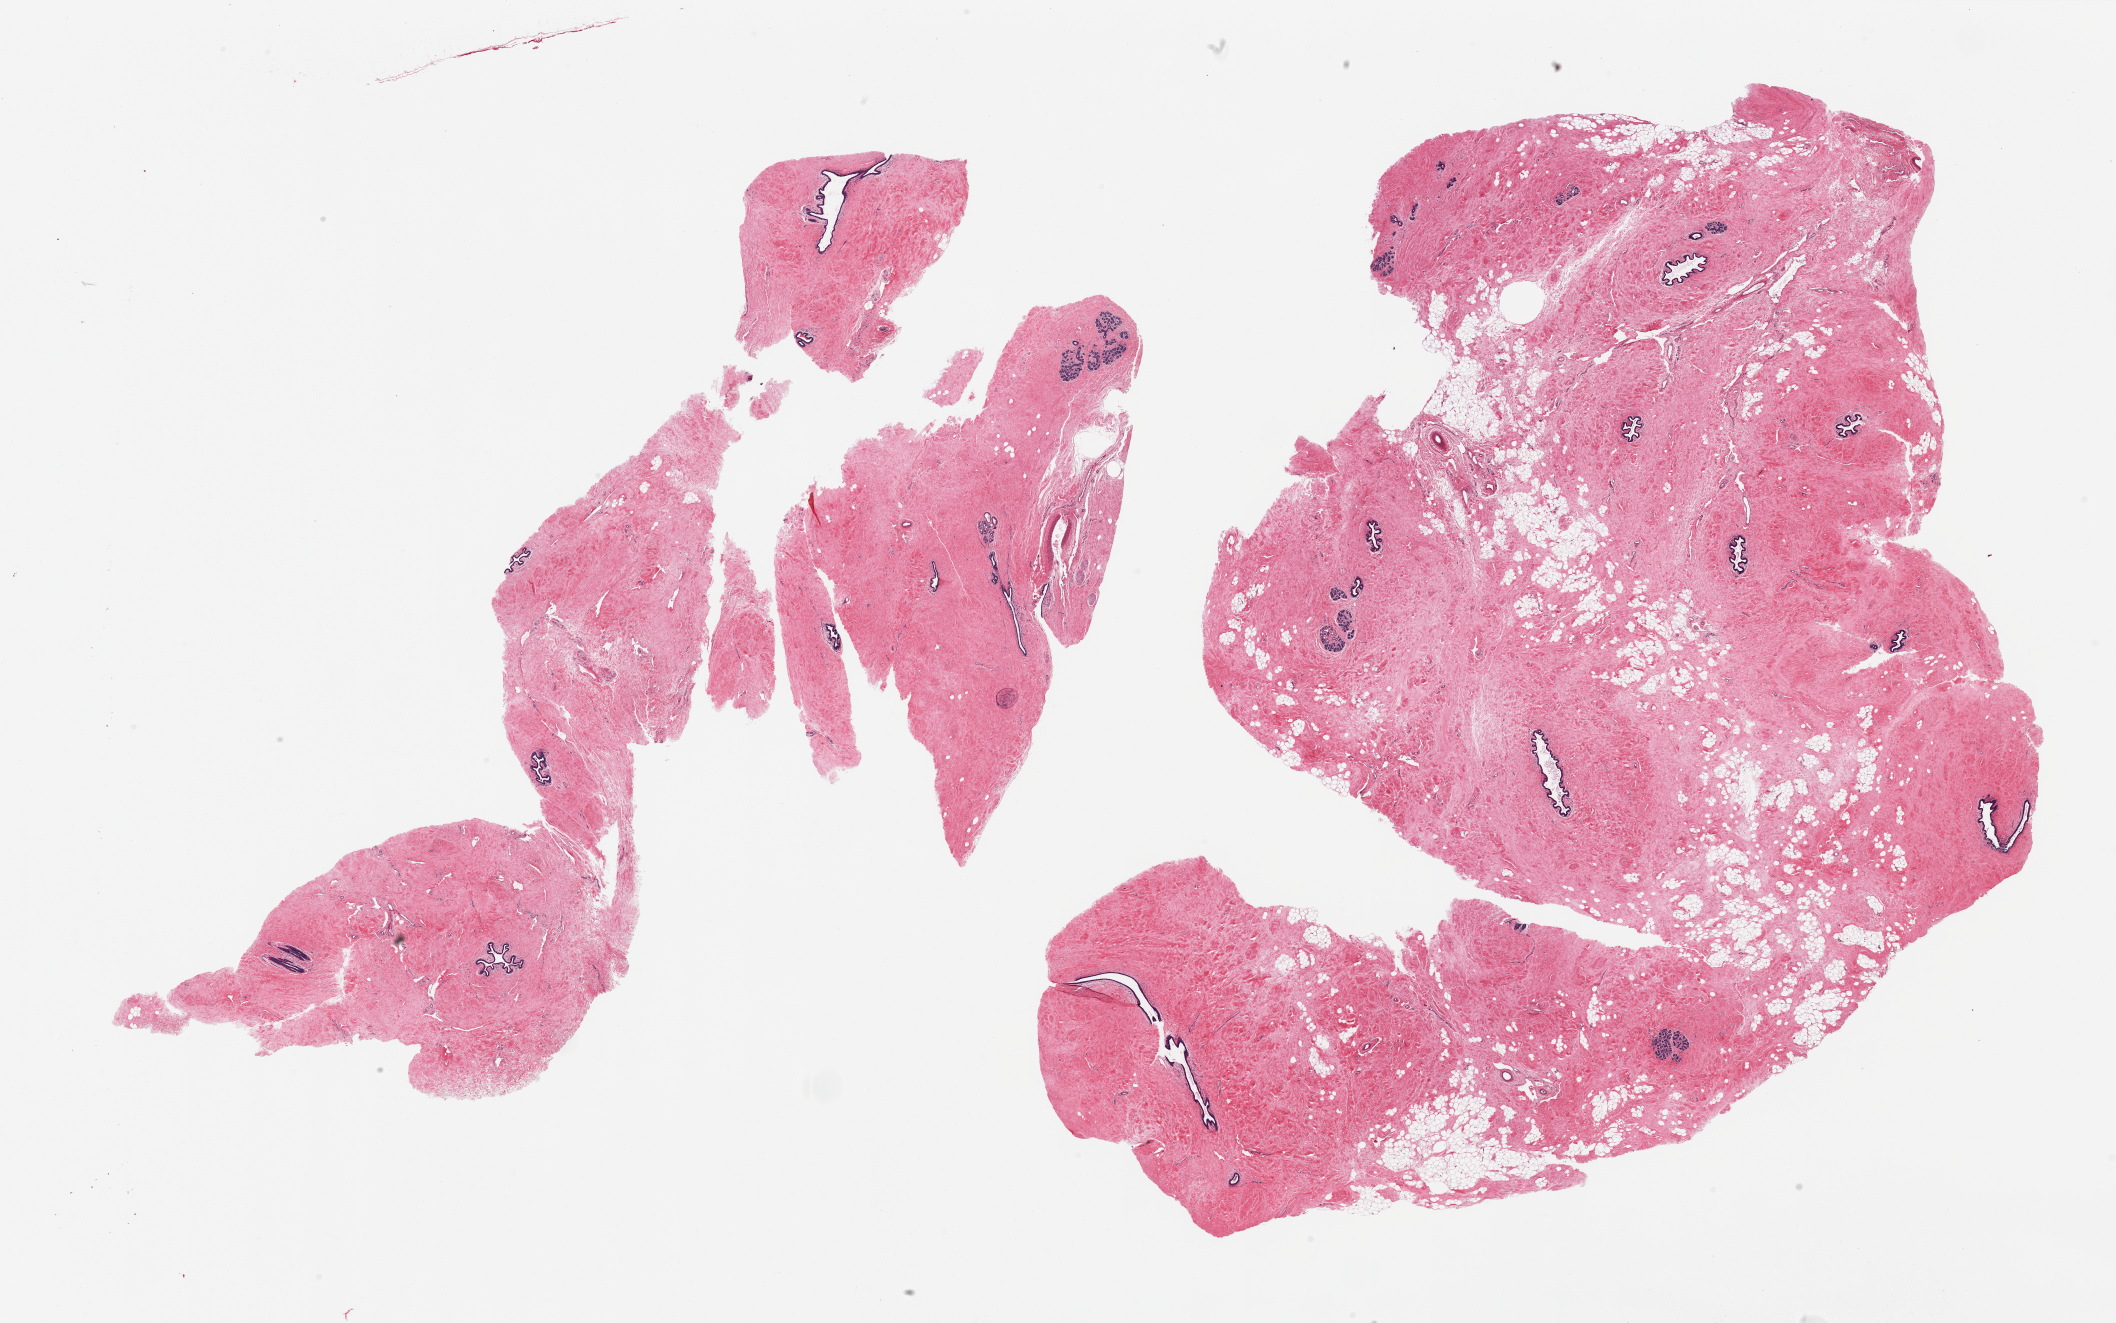
Whole-slide image, H&E stain — shown as a low-resolution overview of the whole scanned area (about 33.5 x 20.9 mm), PAXgene-fixed paraffin-embedded (PFPE) section, sampled site (target tissue): breast, donor tissue sample. Female donor.
• pathologist's review note for this sample: 2 pieces, fibrous mastopathy, normal ductal/lobular elements